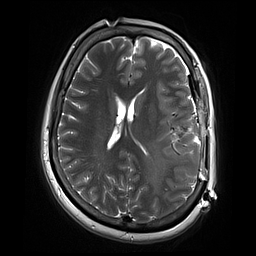
Brain MRI from a brain-tumour surgery series, one axial slice. Slice 32 of 70 in the series (ordered by position). 256 × 256 image matrix, field of view 220 × 220 mm. Case-level facts recorded for this patient, not image findings: histopathology: Glioblastoma; WHO grade: 4; IDH mutation: no; tumour location: Left Temporal.
Annotated regions visible in this slice (manually delineated by an expert):
- residual tumour: box from (x=159, y=116) to (x=174, y=131) px